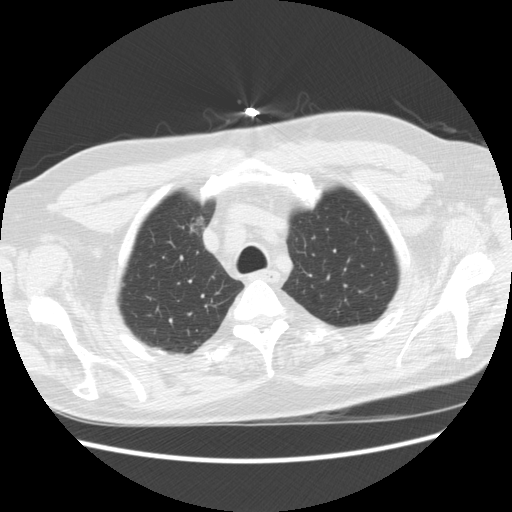
Axial slice from a low-dose chest CT screening exam; baseline annual screen; lung window (W 1500 / L -600 HU); slice 46 of 241 in the series; 512 × 512 image matrix. Male participant, aged 66 years at enrolment. Former smoker at enrolment.
- Expert reader's lesion annotation, box from (x=168, y=209) to (x=212, y=244) px.
- Screening reader's record for this exam: no non-calcified nodule ≥4 mm recorded.
- Later outcome: lung cancer diagnosed 951 days after this screen (after the third annual screen) — bronchiolo-alveolar adenocarcinoma, NOS, right upper lobe, moderately differentiated (G2), stage IA (AJCC 6th edition), 12 mm at pathology.